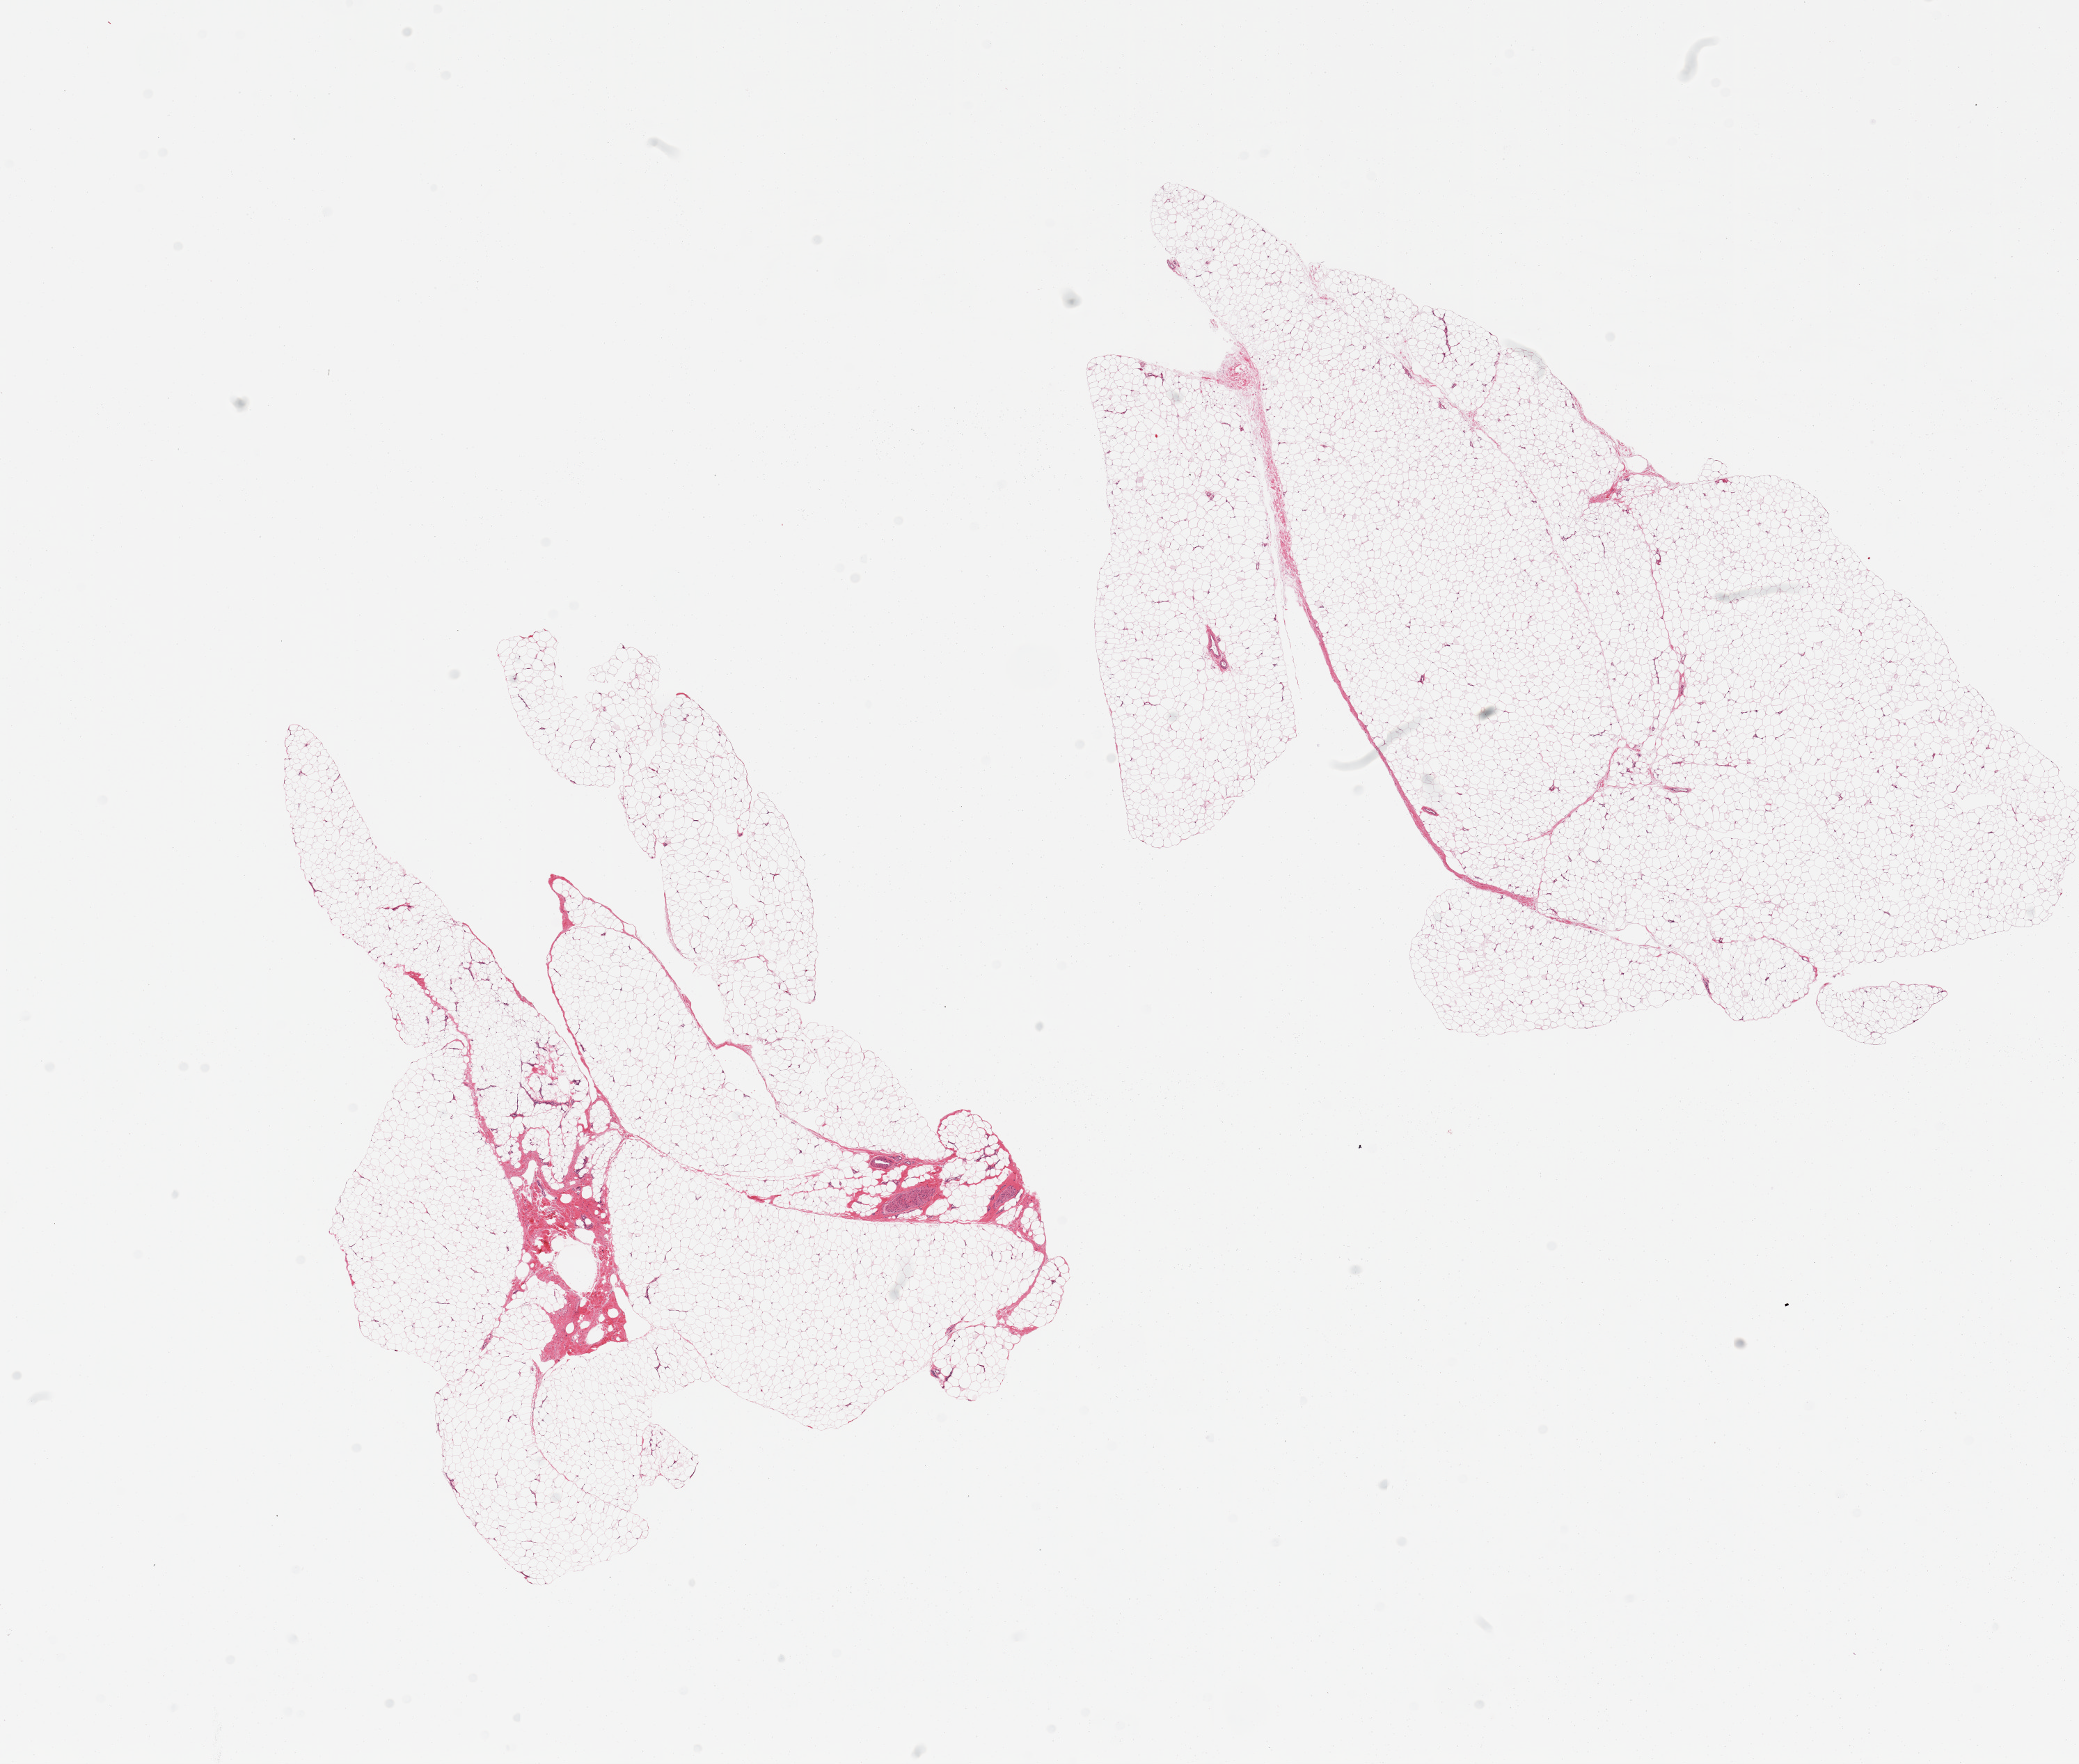
Digitized haematoxylin and eosin-stained section, brightfield, whole scanned area (about 23.6 x 20.0 mm) shown as a low-resolution overview, PAXgene-fixed, paraffin-embedded tissue, target tissue: adipose tissue, donor tissue sample. Male donor.
* pathologist's review note for this sample: 2 pieces